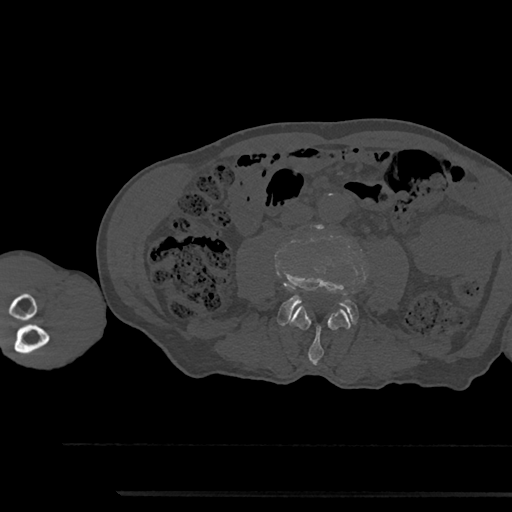
CT including the spine, one axial slice; slice 449 of 797 in the series (ordered by position); reconstruction kernel Br40s/3; 120 kVp; bone window (W 1800 / L 400 HU); 0.5 mm slice thickness; 512 × 512 image matrix, field of view 367 × 367 mm. Patient: male, 79 years. From the clinical record (not read from this slice): primary cancer: prostate.
Outlined on this slice (semi-automatic segmentation, software-assisted and operator-edited):
- L3 vertebra: bounding box [x1, y1, x2, y2] px = [290, 305, 350, 364]
- L4 vertebra: [278, 270, 358, 326]